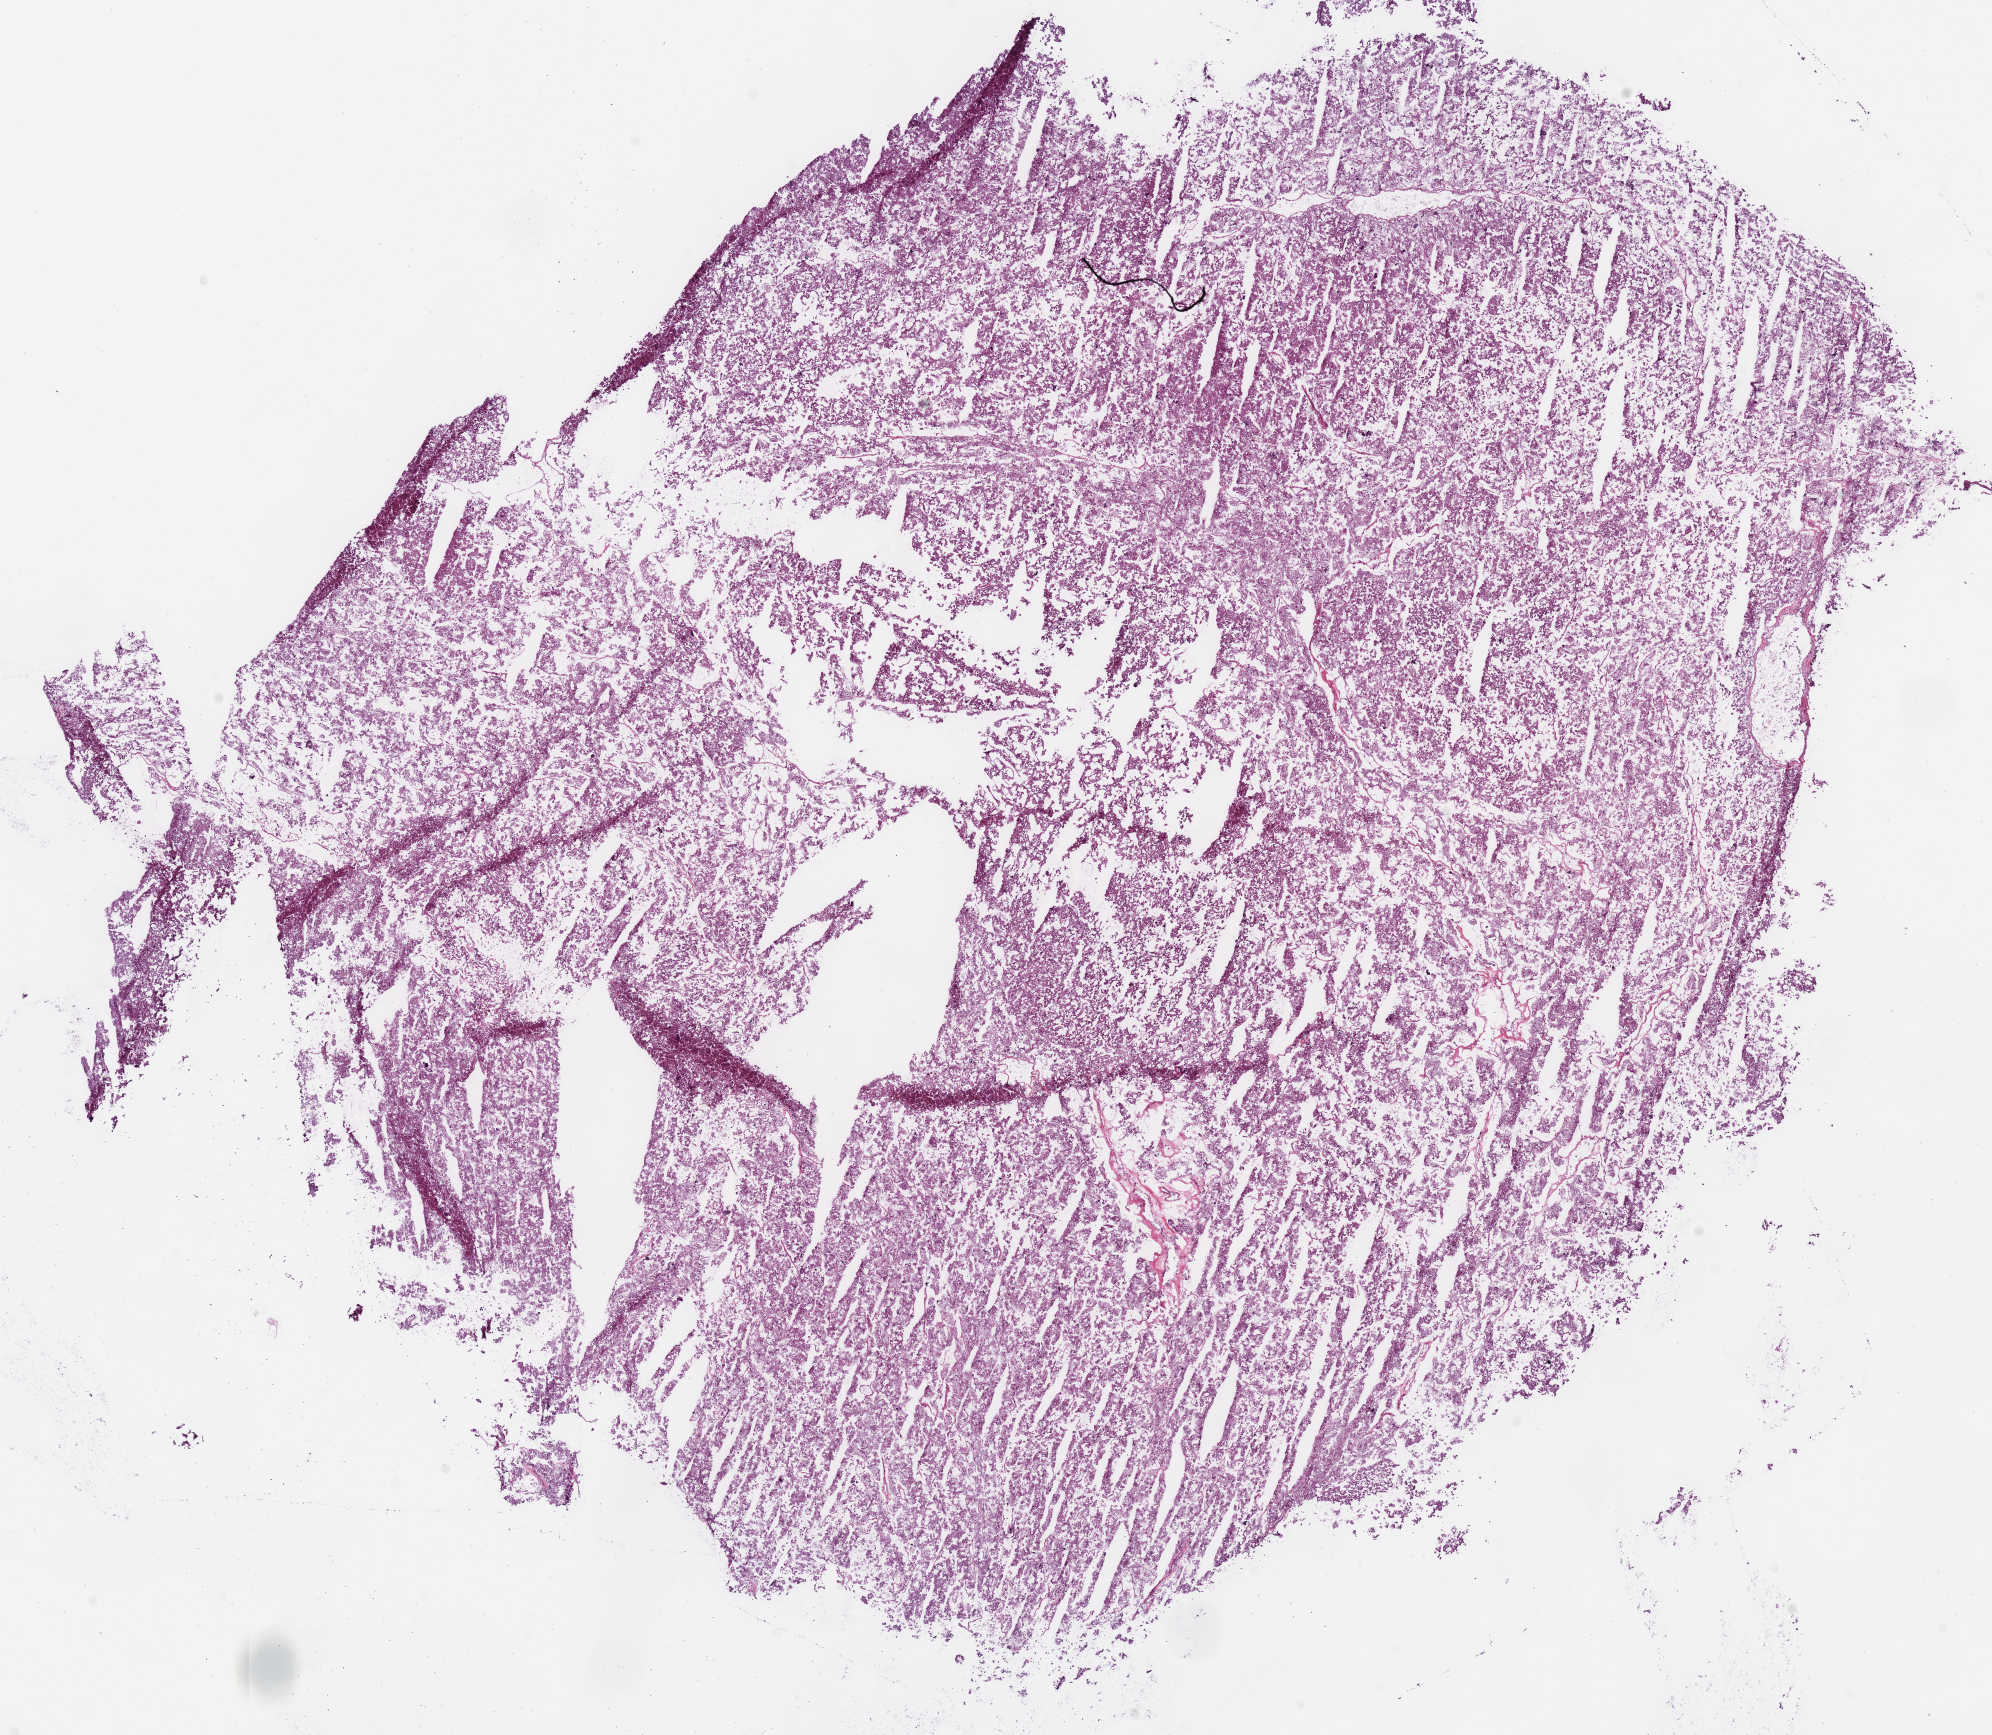
Whole-slide histology image, H&E-stained — whole scanned area (about 15.7 x 13.6 mm) shown as a low-resolution overview, frozen section from the bottom of the tissue portion, kidney, primary tumour sample. Male, age 26 years at initial diagnosis. Composition of this section per pathologist review: tumour cells 95%, tumour nuclei 95%.
Histologic diagnosis: Renal cell carcinoma, chromophobe type.